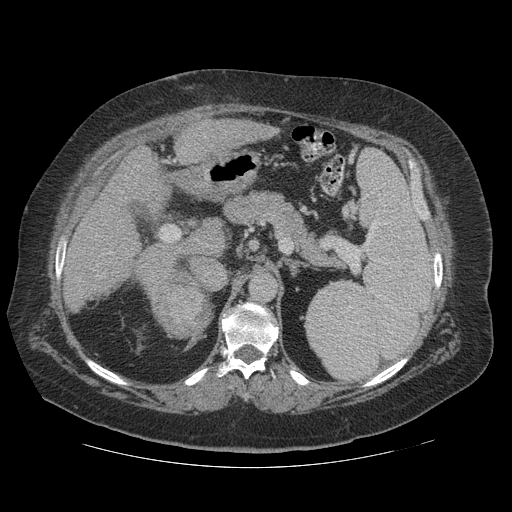
Contrast-enhanced abdominal CT (liver protocol), one axial slice. Slice 68 of 121 in the series (ordered by position). Reconstruction kernel STANDARD. Soft-tissue window (W 400 / L 40 HU). 2.5 mm slice thickness. 512 × 512 image matrix, field of view 420 × 420 mm. Case-level facts recorded for this patient, not image findings: diagnosis: hepatocellular carcinoma (patient treated with transarterial chemoembolisation; whether this scan precedes or follows treatment is not stated here); TNM stage (as recorded): Stage-IIIA; Child-Pugh class: A; tumour differentiation: well differentiated.
Outlined on this slice (semi-automatic segmentation, software-assisted and operator-edited):
- liver parenchyma outside the tumour (the mass and vessels are separate outlines, so this box may not span the whole liver): bounding box <68,120,278,282> (left, top, right, bottom; pixels)
- mass: <152,271,213,337>
- liver vessels: <96,235,112,278>